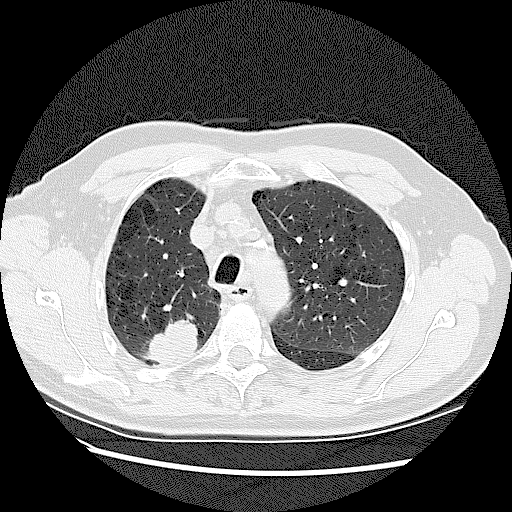
Low-dose screening chest CT, one axial slice. Position 96 of 128 along the scan axis. 120 kVp. Lung window (W 1500 / L -600 HU). 2.5 mm slice thickness. 512 × 512 image matrix, field of view 360 × 360 mm.
Outlined on this slice (outlined manually by an expert reader):
- lesion 2 (tumor, upper lobe of right lung): box from (x=148, y=320) to (x=197, y=365) px